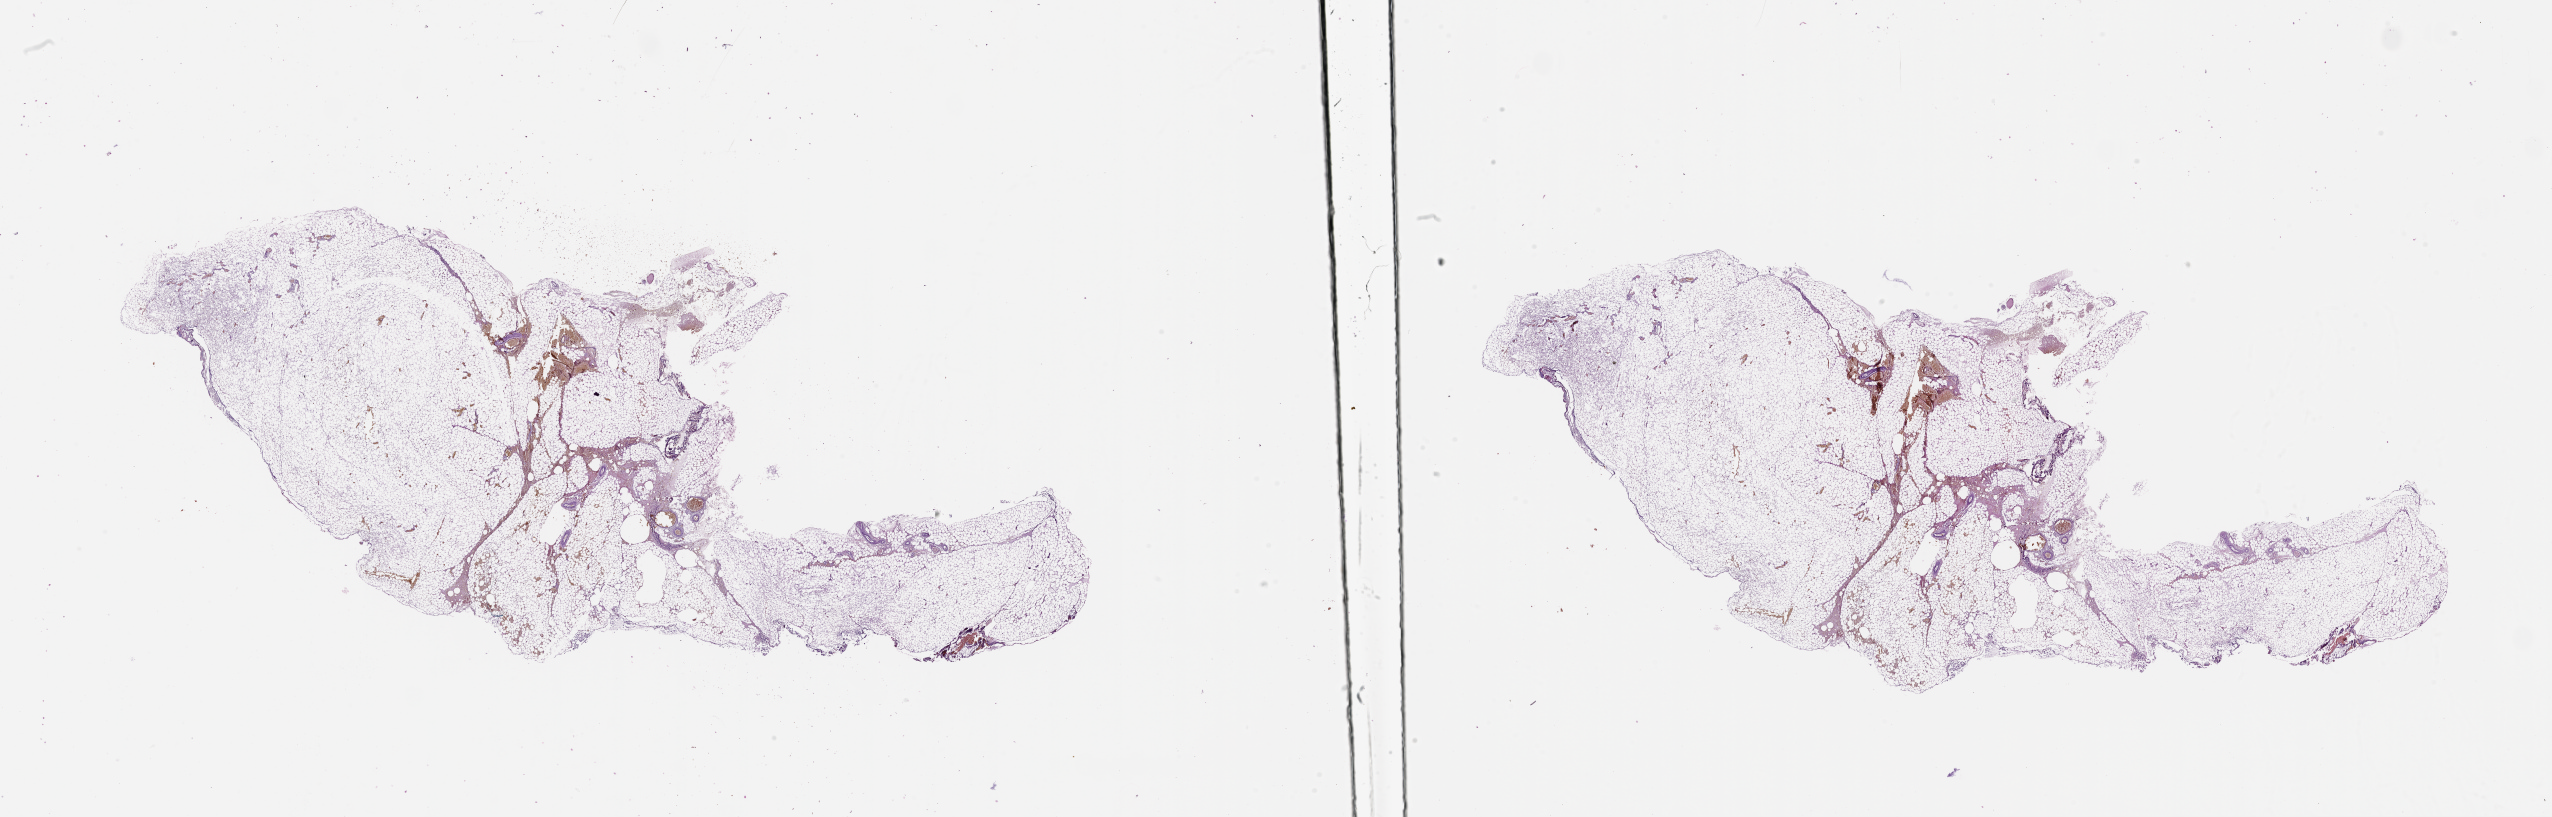
Whole-slide histology image, H&E — whole scanned area (about 41.1 x 13.2 mm) shown as a low-resolution overview, normal (non-tumour) tissue sample, sampled site: trunk. 47-year-old male patient.
This section: normal (non-tumour) tissue from the same patient. Patient diagnosis: Malignant melanoma, NOS.